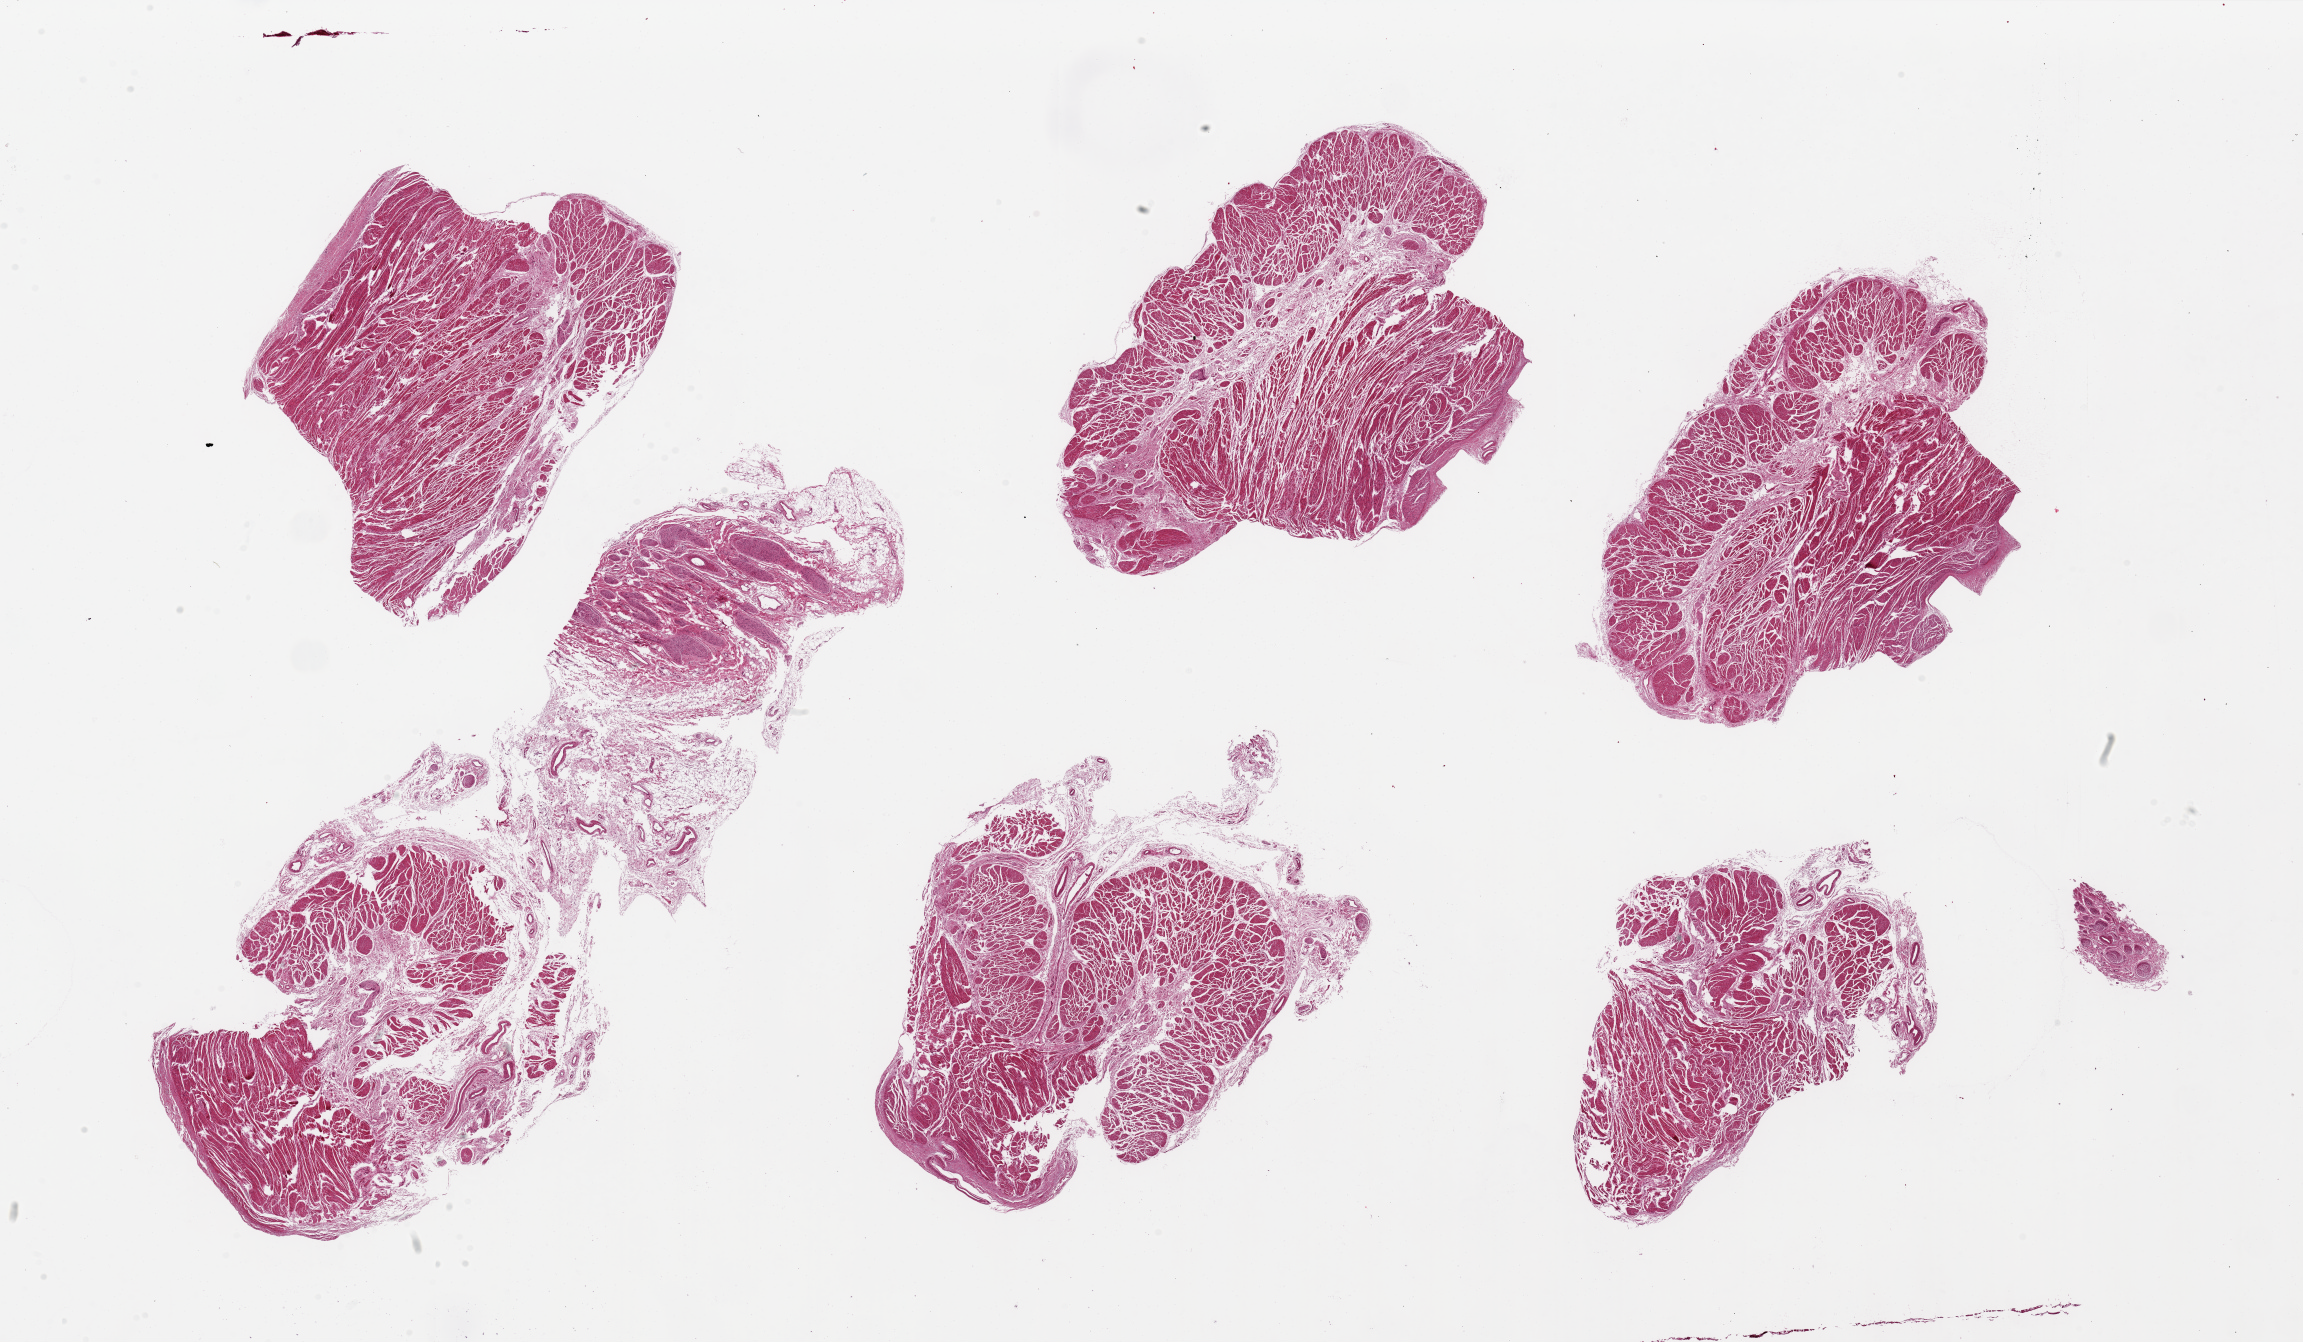
Digitized H&E-stained section — low-resolution overview of the scanned area, about 36.4 x 21.2 mm, PAXgene-fixed, paraffin-embedded tissue, section of gastroesophageal junction (target tissue), donor tissue sample. Female donor.
Review note (as recorded): 6 pieces, up to 15x6mm; 5 muscularis (target); 1 muscle and fibrous stroma.